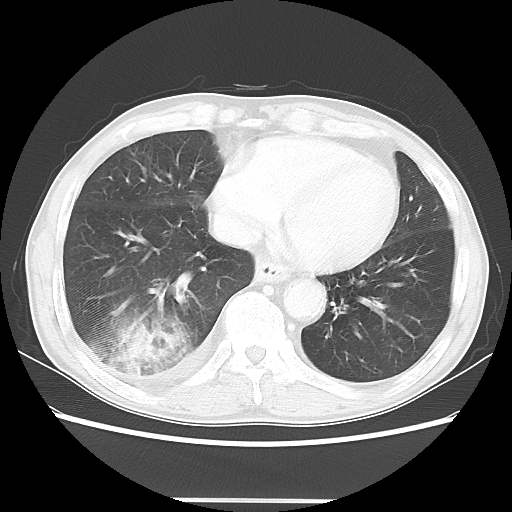
Chest CT, one axial slice; slice 12 of 48 in the series (ordered by position); lung window (W 1500 / L -600 HU); 5 mm slice thickness; 512 × 512 image matrix, field of view 361 × 361 mm. Patient: male, 66 years. Case-level facts recorded for this patient, not image findings: clinical TNM (as recorded): T4 N1 M1; histopathological grade: G3.
Annotated regions visible in this slice (bounding box drawn by a radiologist):
- lung tumour (recorded histology: small cell carcinoma): bounding box [x1, y1, x2, y2] px = [81, 309, 195, 387]